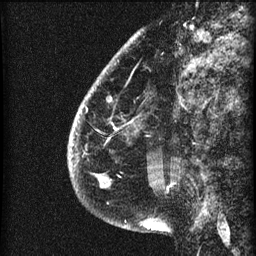
Breast MRI (dynamic contrast-enhanced), one sagittal slice; position 14 of 60 along the scan axis; 3 images stored at this slice position (order not interpretable as contrast timing); 1.5 T; TE 4.2 ms, TR 22.7 ms; 256 × 256 image matrix, field of view 180 × 180 mm. Female patient, age 48 years. Case-level facts recorded for this patient, not image findings: setting: breast cancer imaged before/during neoadjuvant chemotherapy; receptor status: triple-negative.
Structures marked on this image (semi-automatically segmented with operator editing):
- analysis volume of interest (the breast-tissue region the enhancement analysis was run in; not a lesion): bounding box (x1, y1, x2, y2) in pixels: (69, 30, 173, 207)
- tumour enhancement mask (voxels above the 90 % enhancement threshold inside the analysis volume of interest): (70, 154, 110, 188)